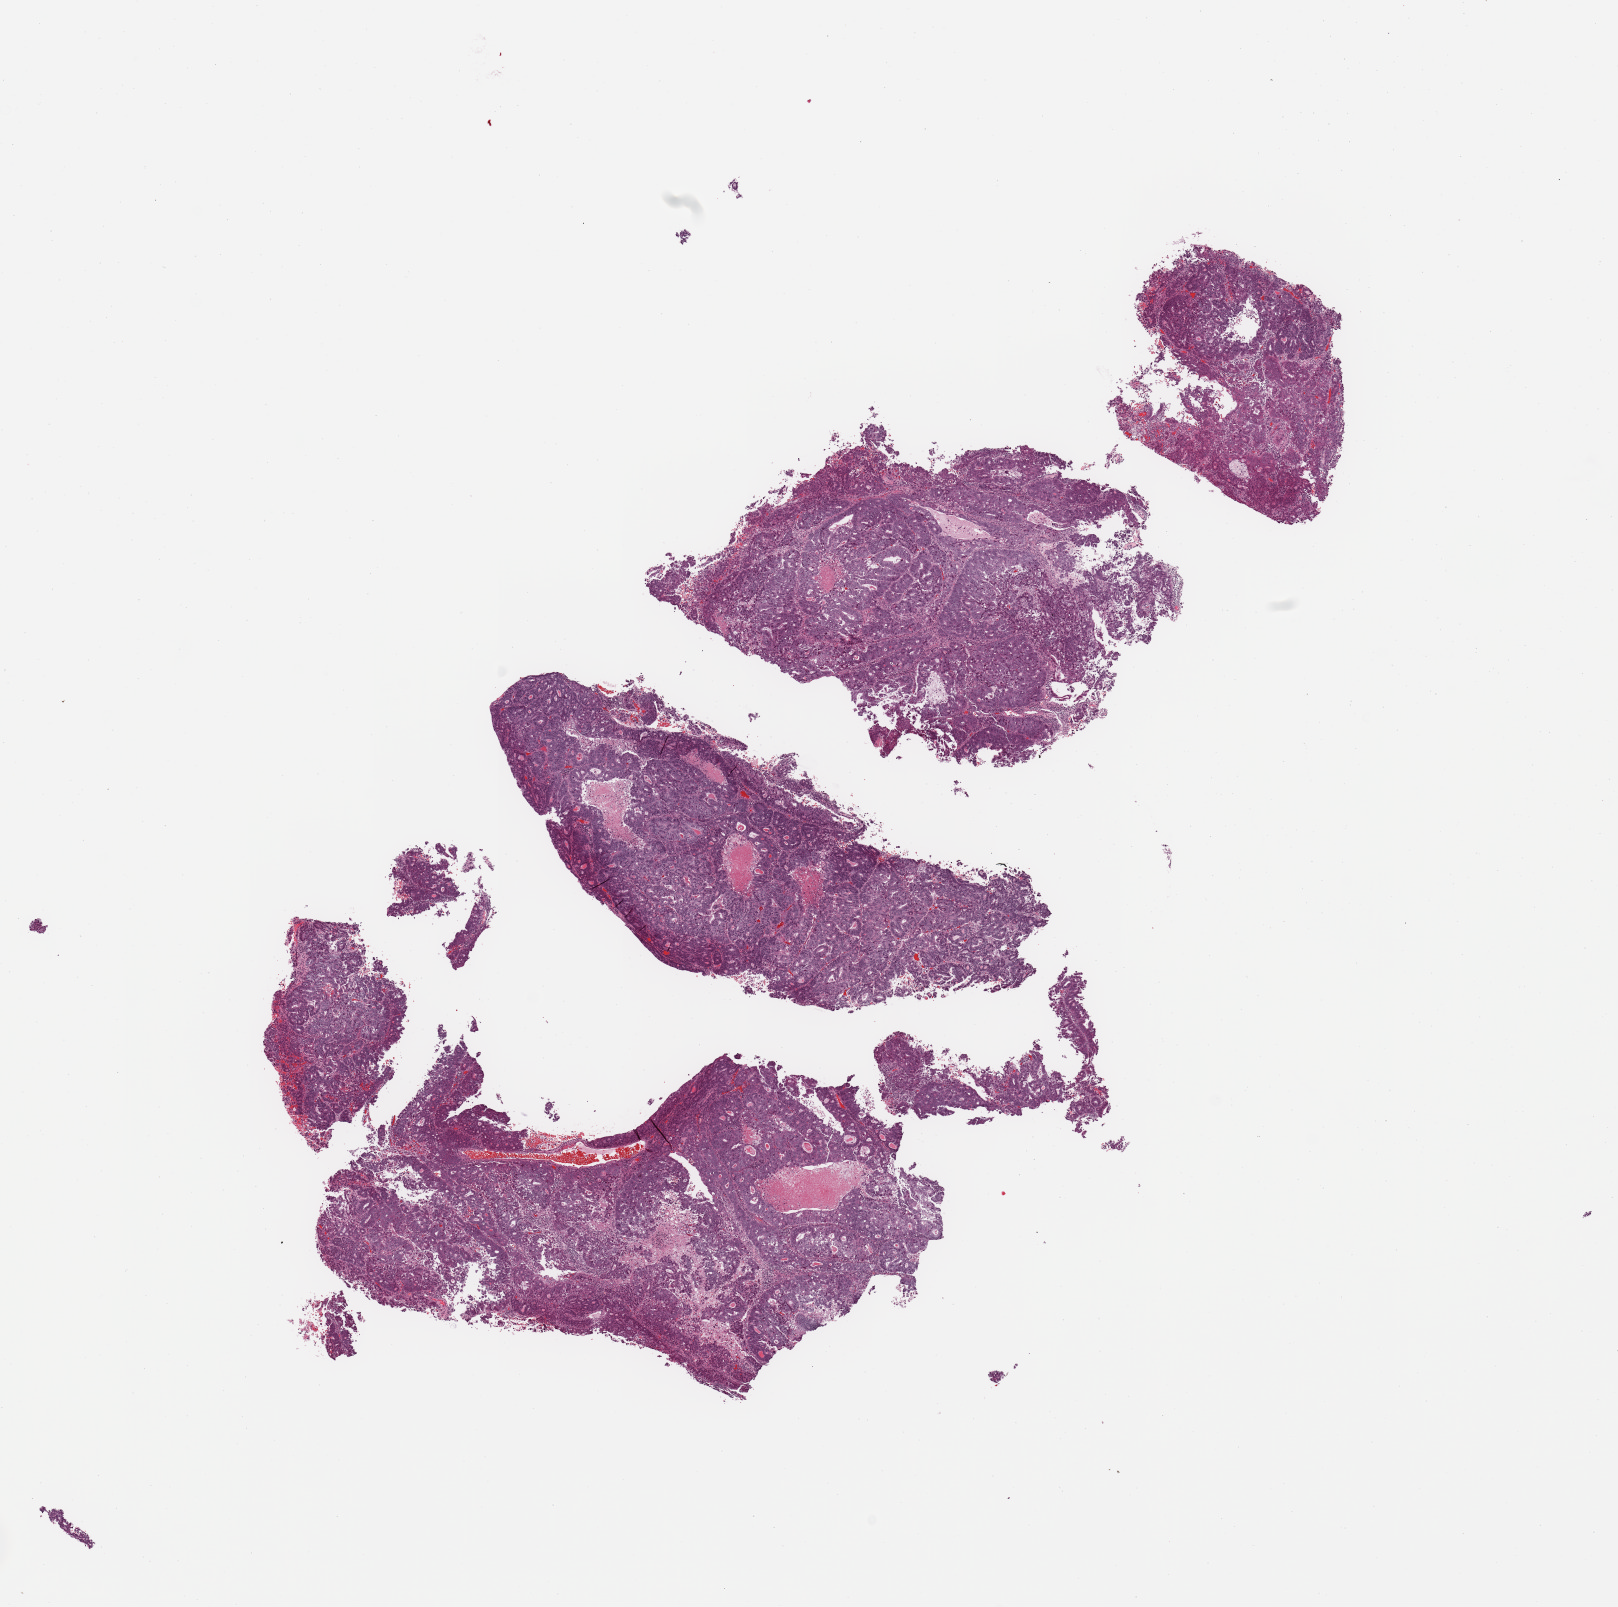
Whole-slide histology image, H&E-stained, whole scanned area (about 12.8 x 12.7 mm, acquisition: 20x scan) shown as a low-resolution overview, uterus, tissue type not recorded.
• patient diagnosis (cohort enrolment): corpus endometrial carcinoma (uterus)